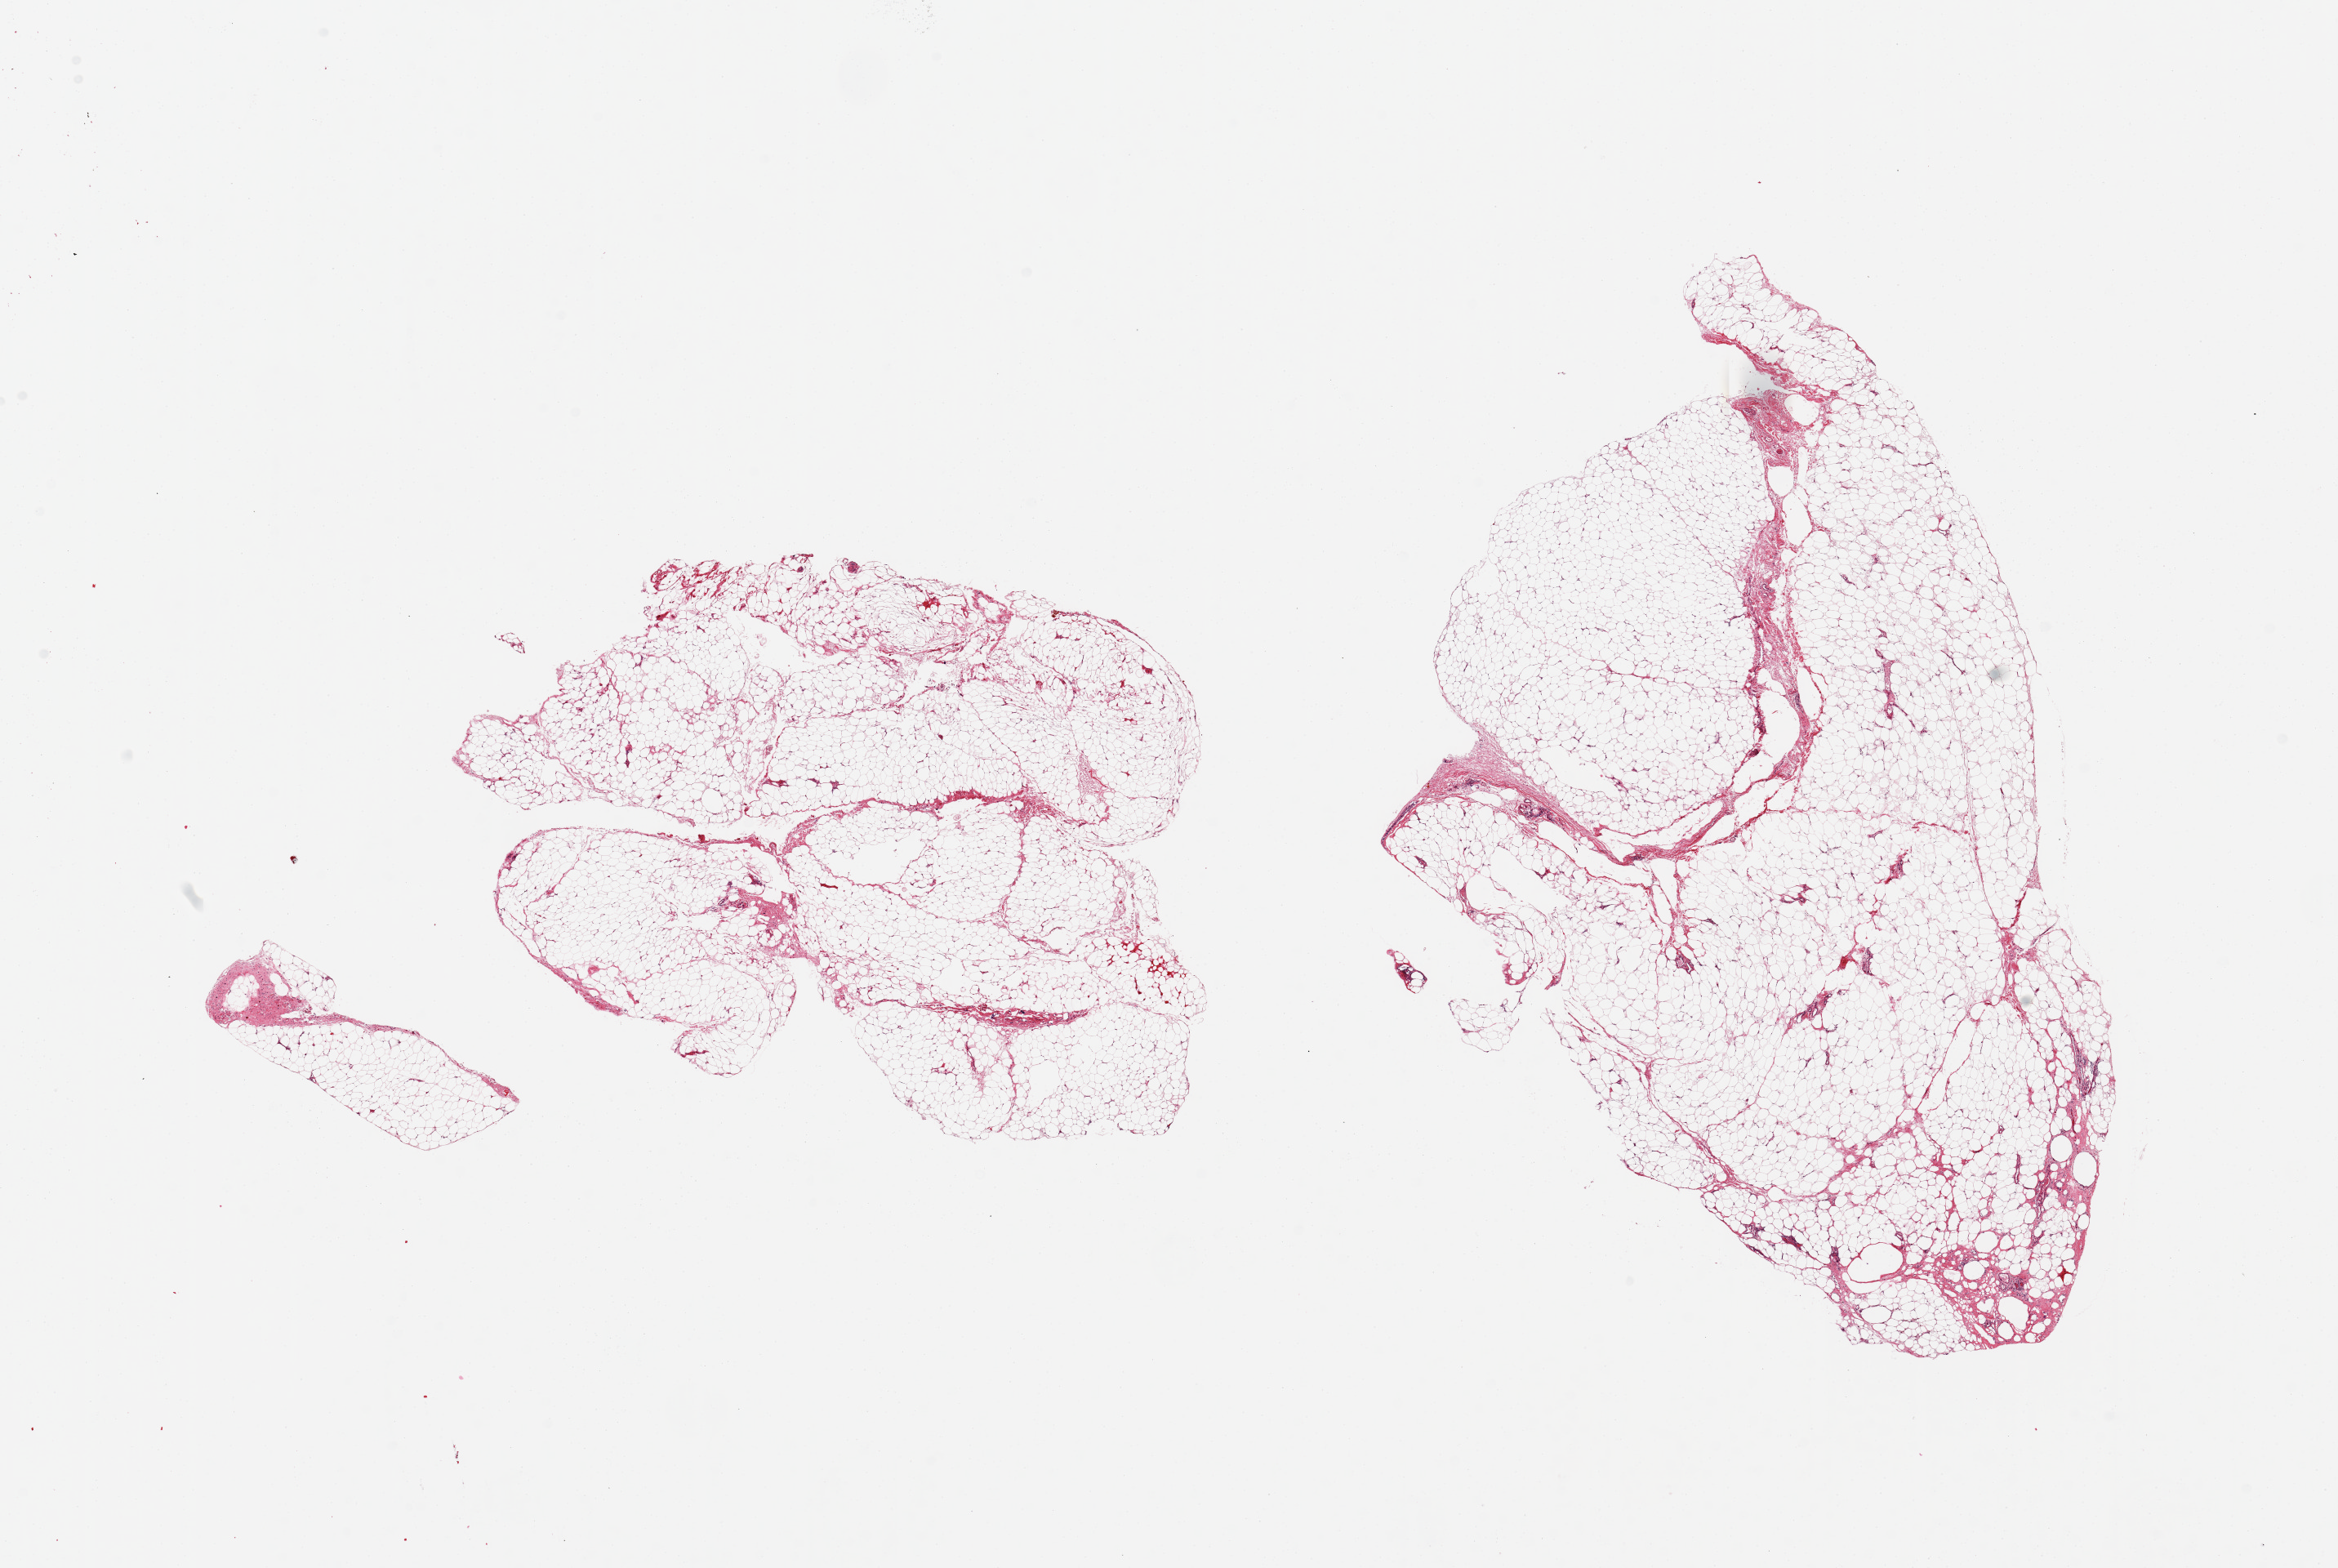
Whole-slide image, H&E stain — a low-resolution overview of the entire scanned area, about 22.6 x 15.2 mm, PAXgene-fixed, paraffin-embedded tissue, sampled site (target tissue): omentum, tissue donor sample. Donor sex: female.
Pathologist's review note for this sample: 2 pieces, ~10% vascular/mesothelial tissue.